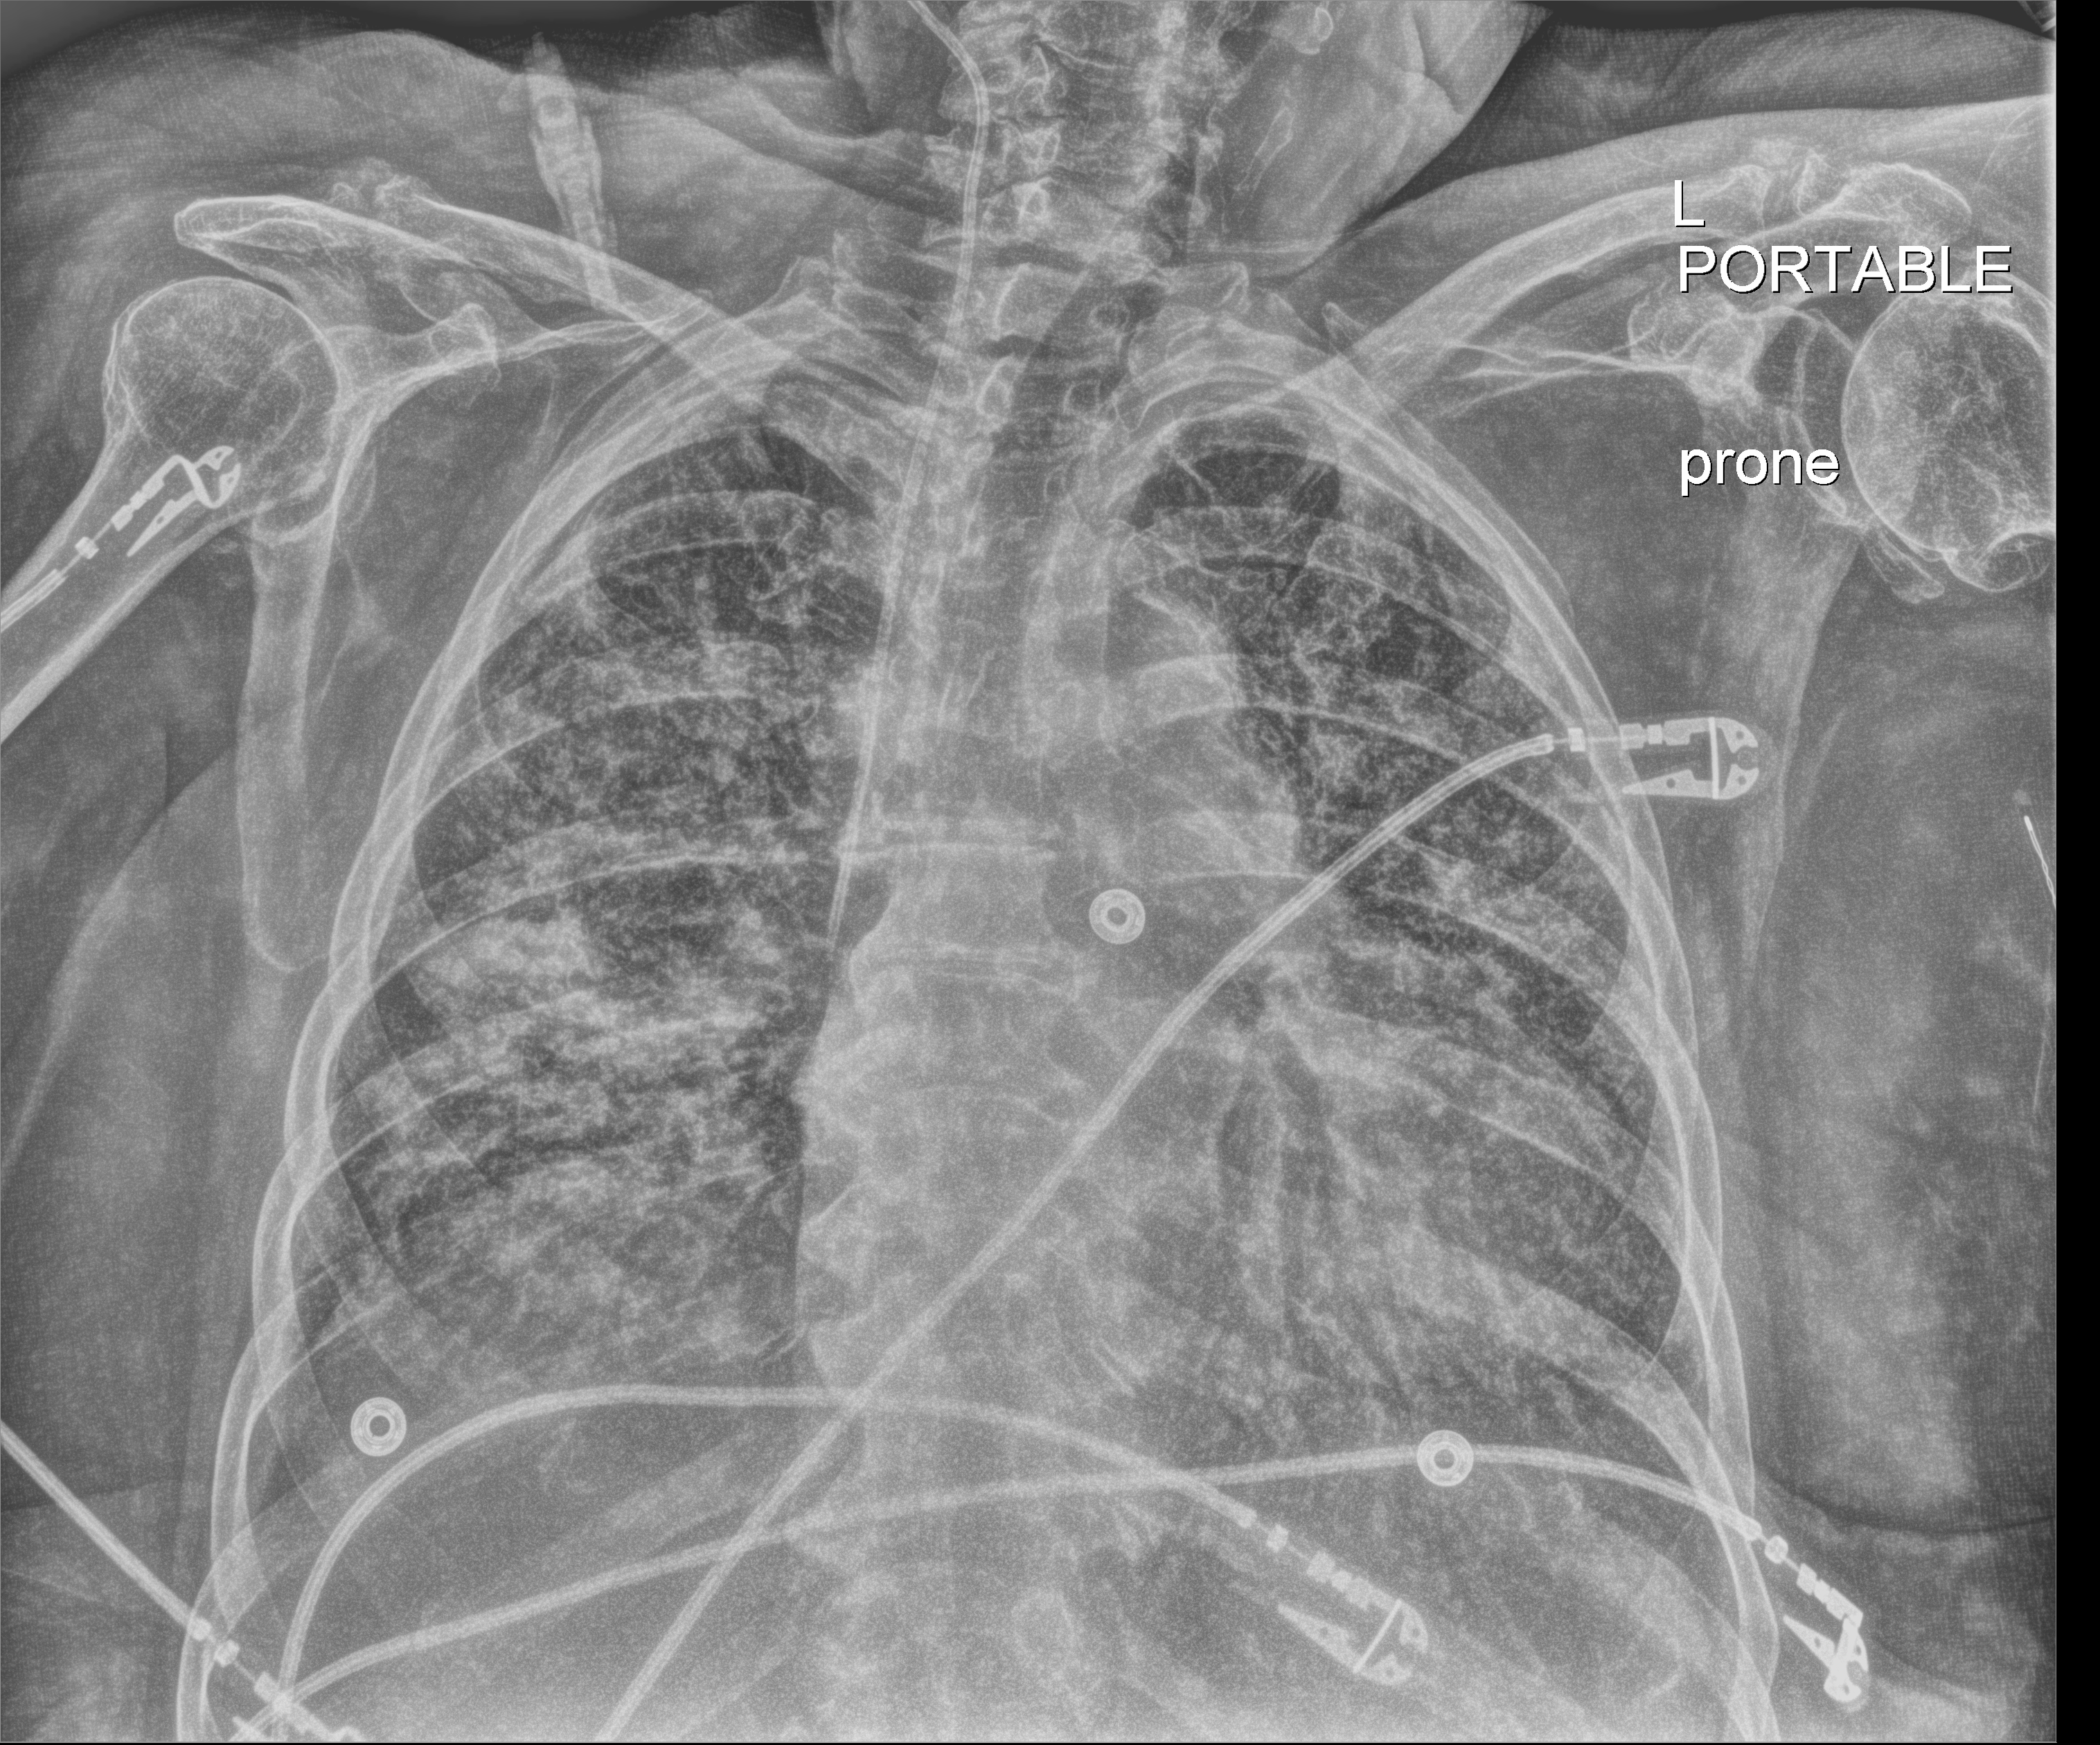
Chest X-ray (portable); anteroposterior (AP) projection. Patient hospitalised with COVID-19; female, aged 75–90 years.
From the hospital-stay record, not from the radiograph (when in the stay this image was taken is not recorded):
- length of hospital stay: 56 days